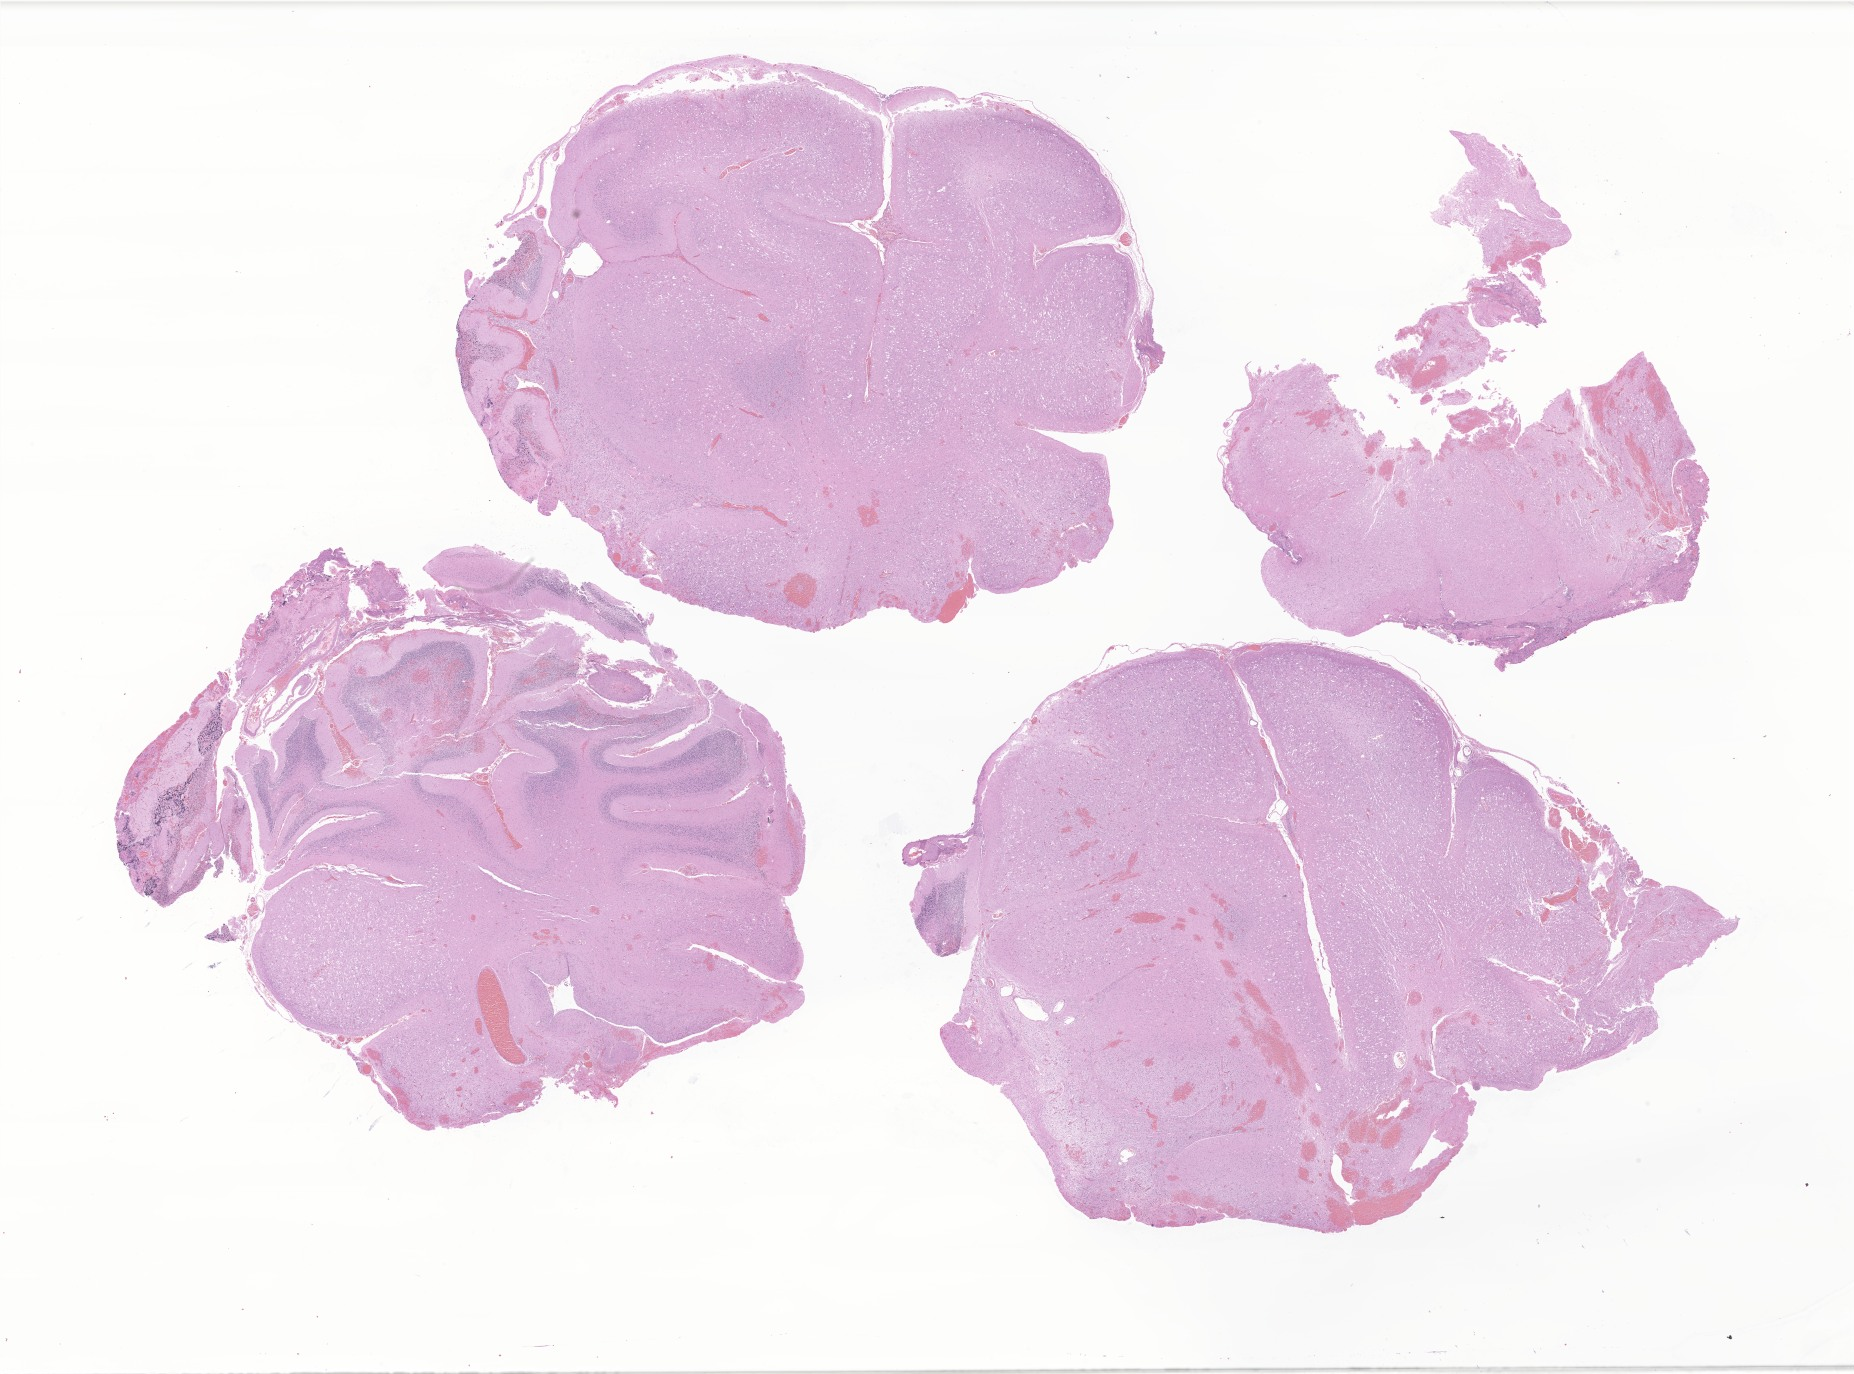
Whole-slide image, hematoxylin and eosin (H&E) stain of tumor tissue from the cerebellum — shown as a low-resolution overview of the whole scanned area (about 31.3 x 23.2 mm); FFPE section. Patient female; age 126 months (10 years 6 months).
Diagnosis (ICD-O-3 morphology term): Ganglioglioma, NOS.